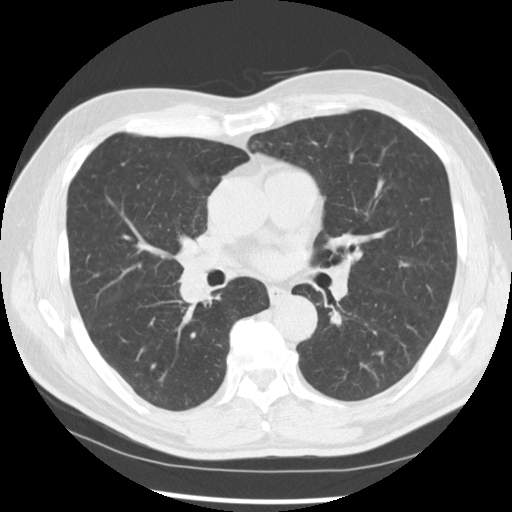
Low-dose screening chest CT, one axial slice. Position 153 of 277 along the scan axis. Reconstruction kernel STANDARD. 120 kVp. Lung window (W 1500 / L -600 HU). 2.5 mm slice thickness. 512 × 512 image matrix, field of view 365 × 365 mm.
Structures marked on this image (manually delineated by an expert):
- lesion 1 (tumor, middle lobe of right lung): bounding box [x1, y1, x2, y2] px = [177, 268, 210, 305]